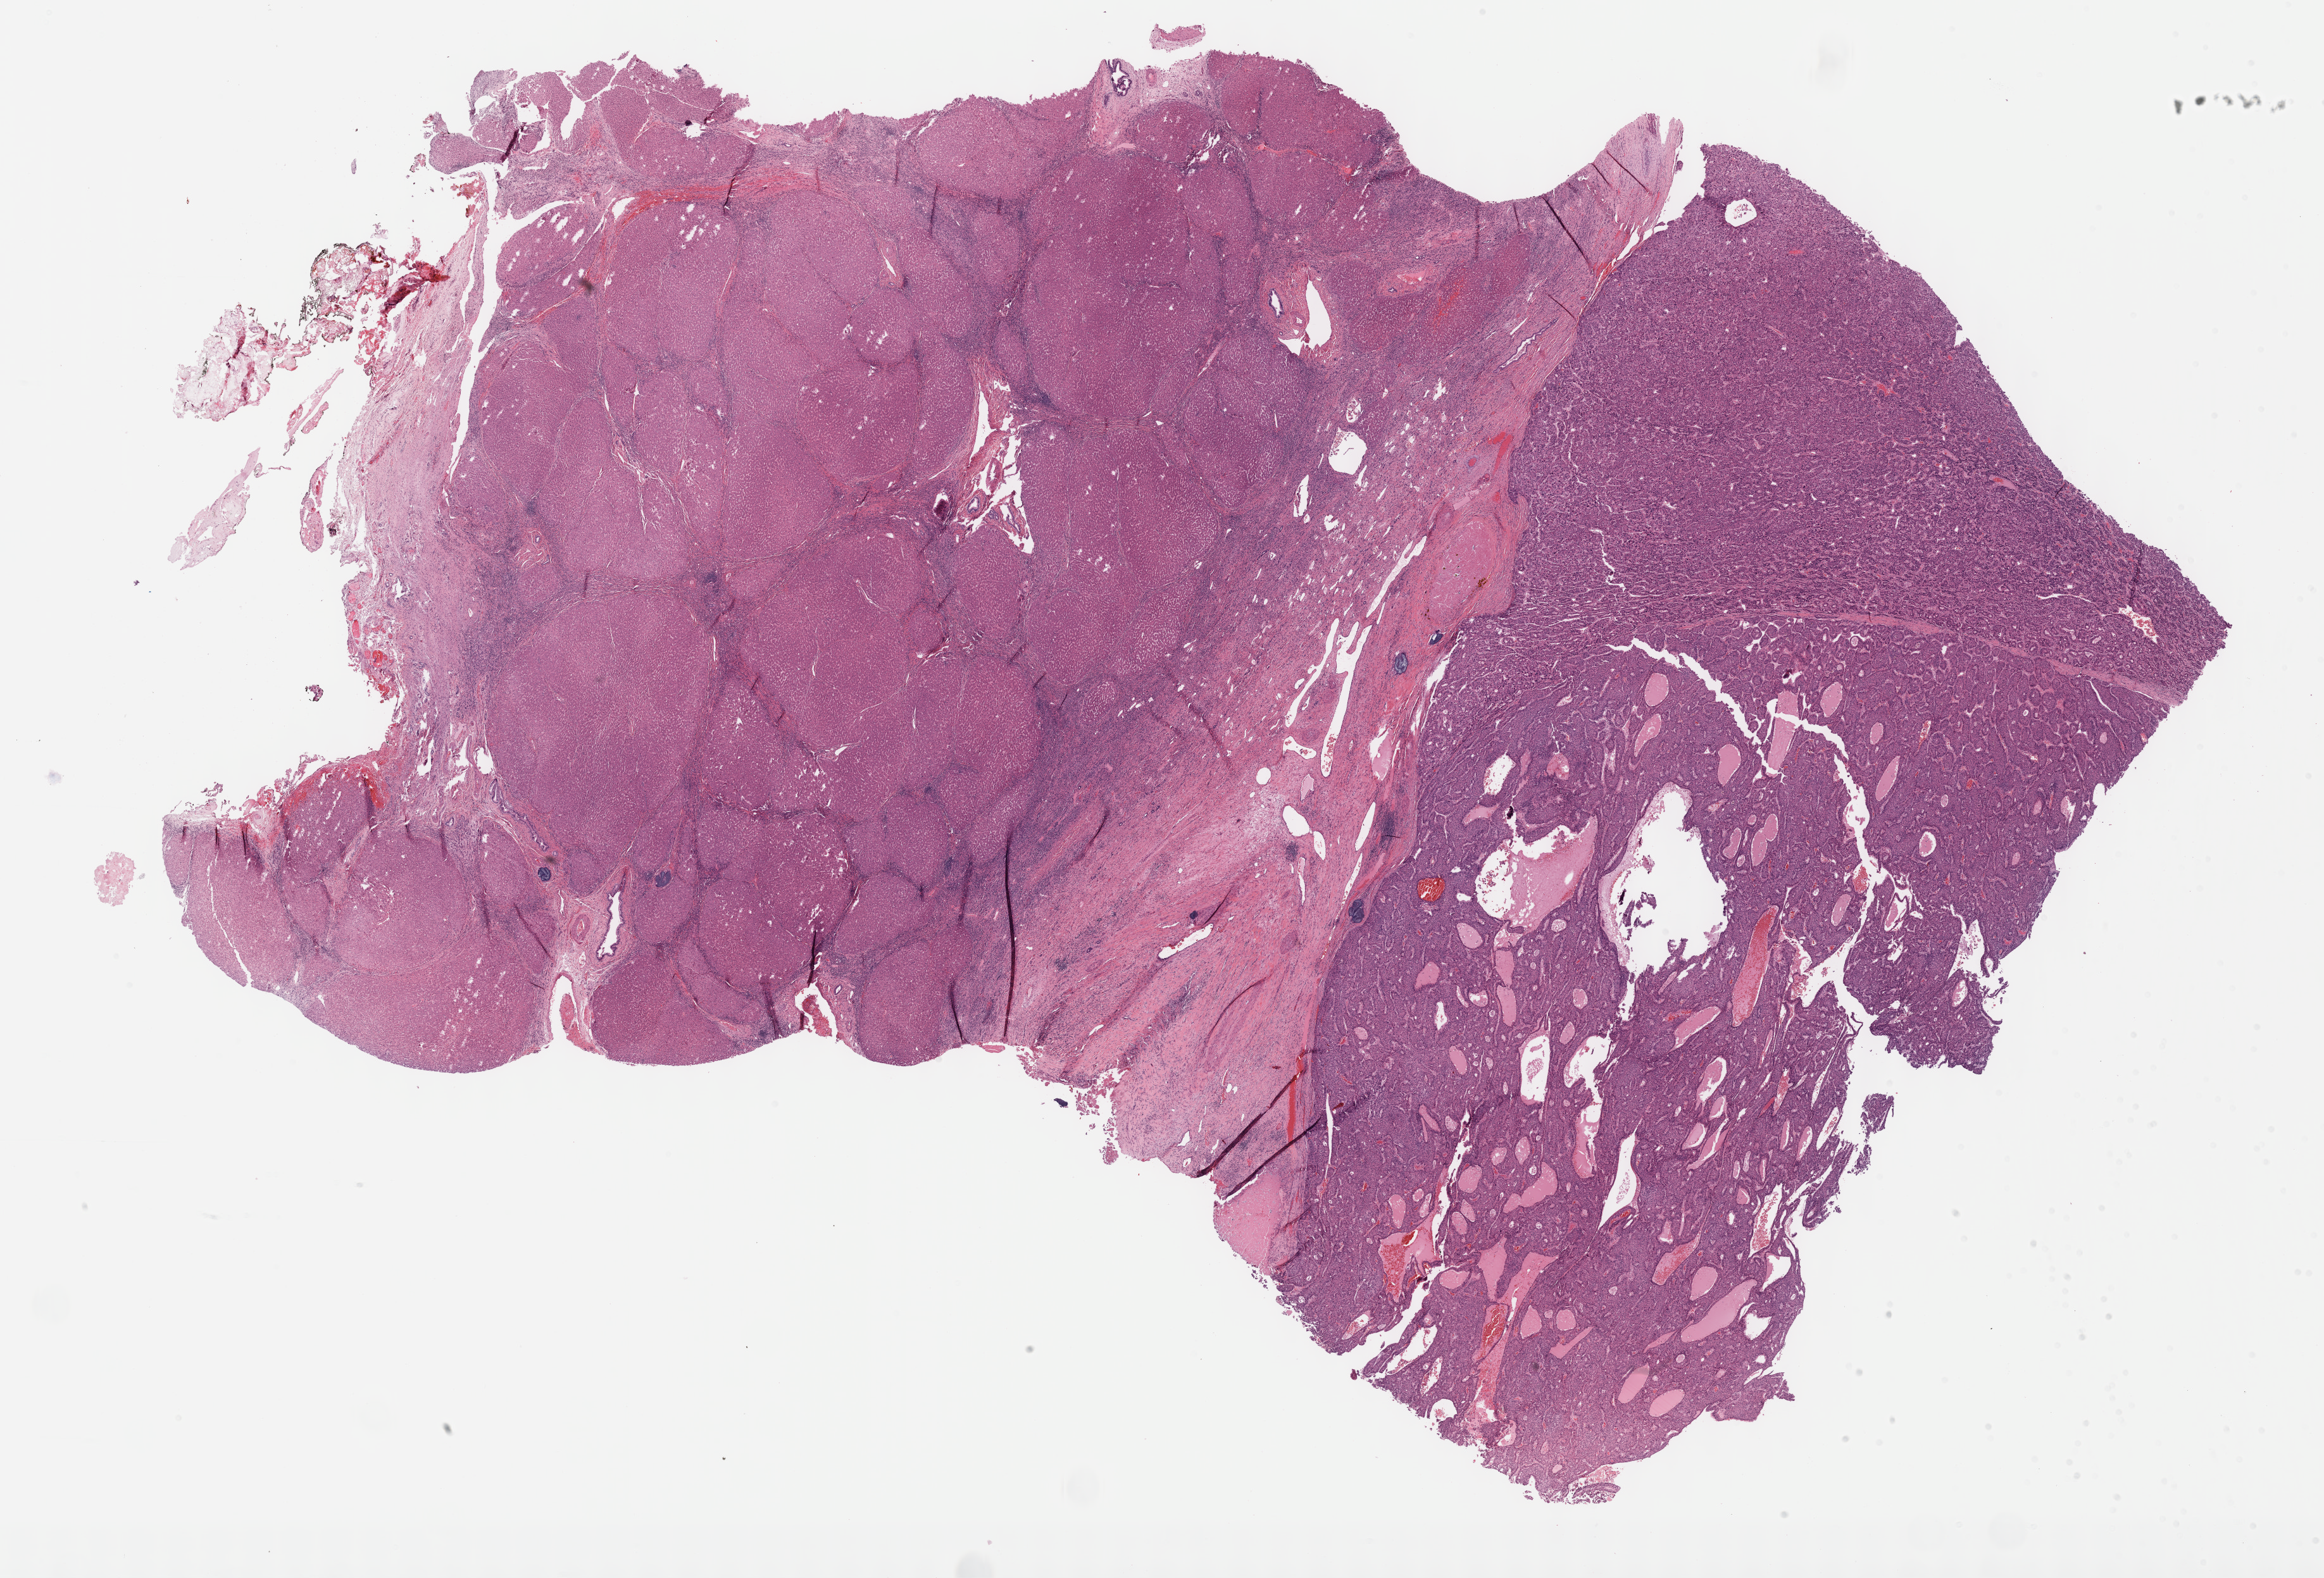
Digitized Hematoxylin and eosin (H&E) stained tissue section (whole slide), low-resolution overview of the scanned area, about 29.7 x 20.2 mm (acquisition: 40x scan), formalin-fixed paraffin-embedded (FFPE) diagnostic section, liver, primary tumour sample. Male patient; age at initial diagnosis 63 years. Histologic grade: G2 (moderately differentiated).
AJCC pathologic stage: II. Histologic diagnosis: Hepatocellular carcinoma, NOS. TNM: T2 N0 M0.